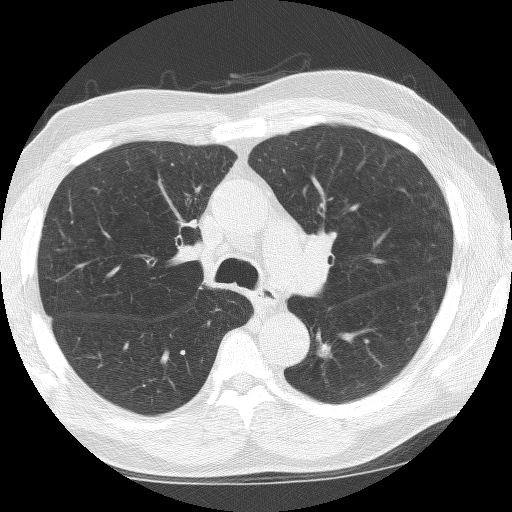
Low-dose screening chest CT, one axial slice; slice 97 of 155 in the series (ordered by position); reconstruction kernel BONE; 120 kVp; lung window (W 1500 / L -600 HU); 2.5 mm slice thickness; 512 × 512 image matrix, field of view 323 × 323 mm.
Structures marked on this image (expert manual segmentation):
- lesion 1 (tumor, lower lobe of left lung): bounding box <316,329,332,358> (left, top, right, bottom; pixels)